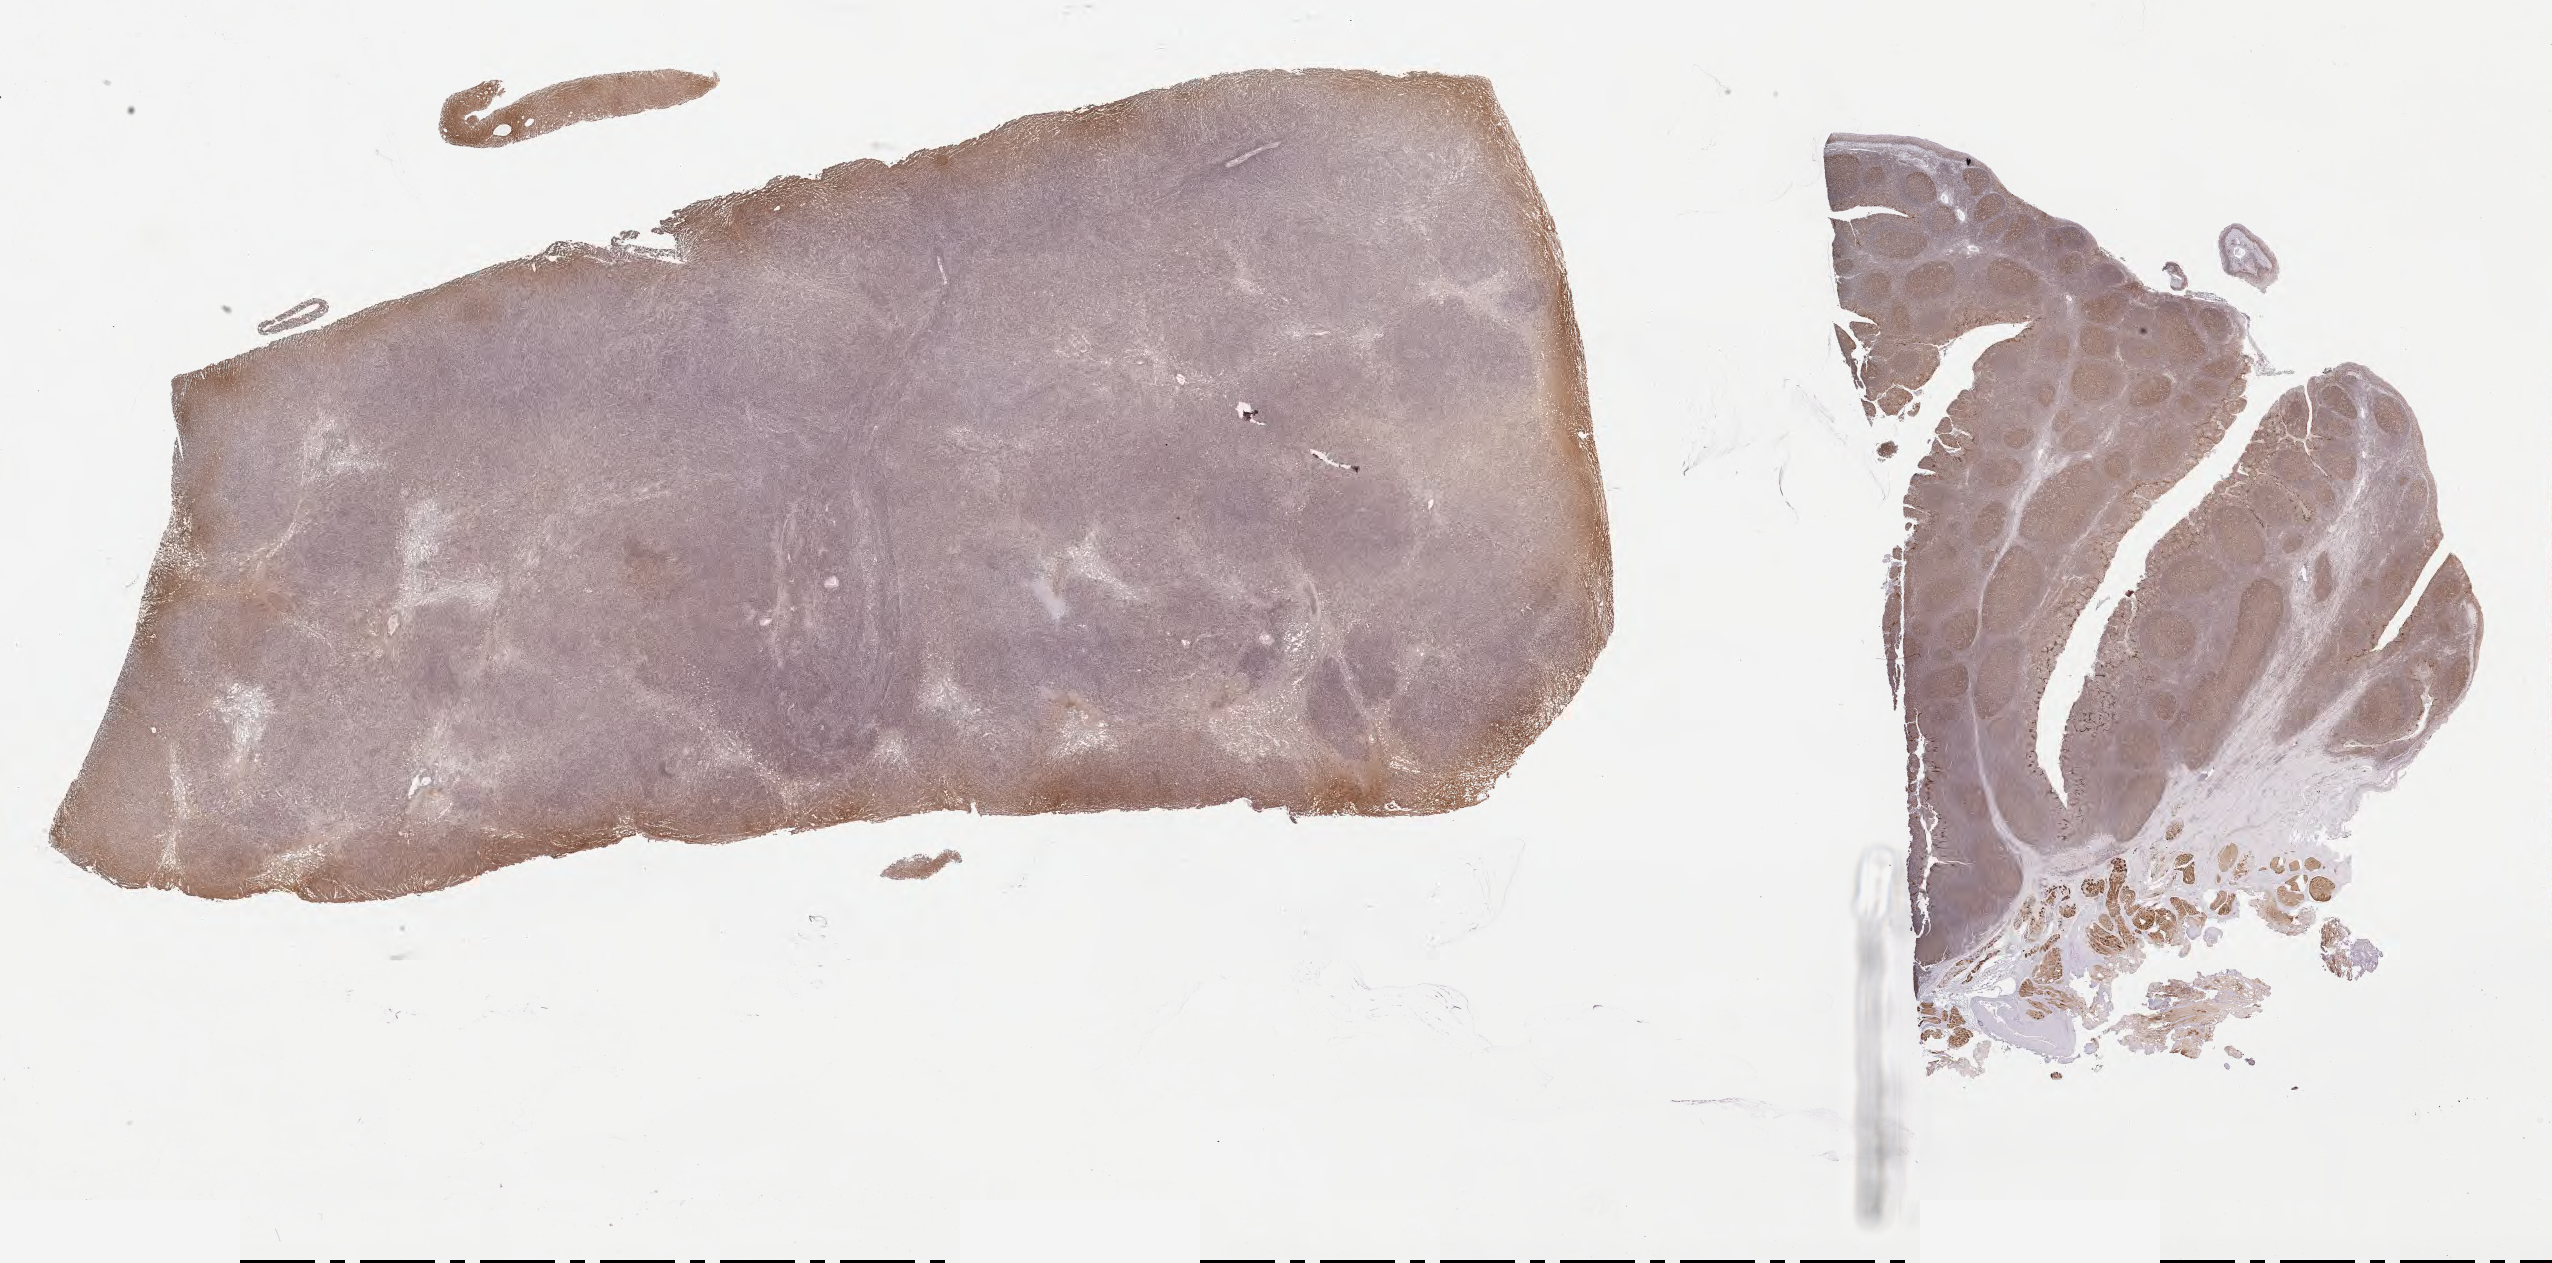
IHC for BCL6, whole-slide image, a low-resolution overview of the entire scanned area, about 41.3 x 20.4 mm; specimen: tumor tissue. Patient male; age 39 years.
Histologic diagnosis: Diffuse large B-cell lymphoma, NOS.